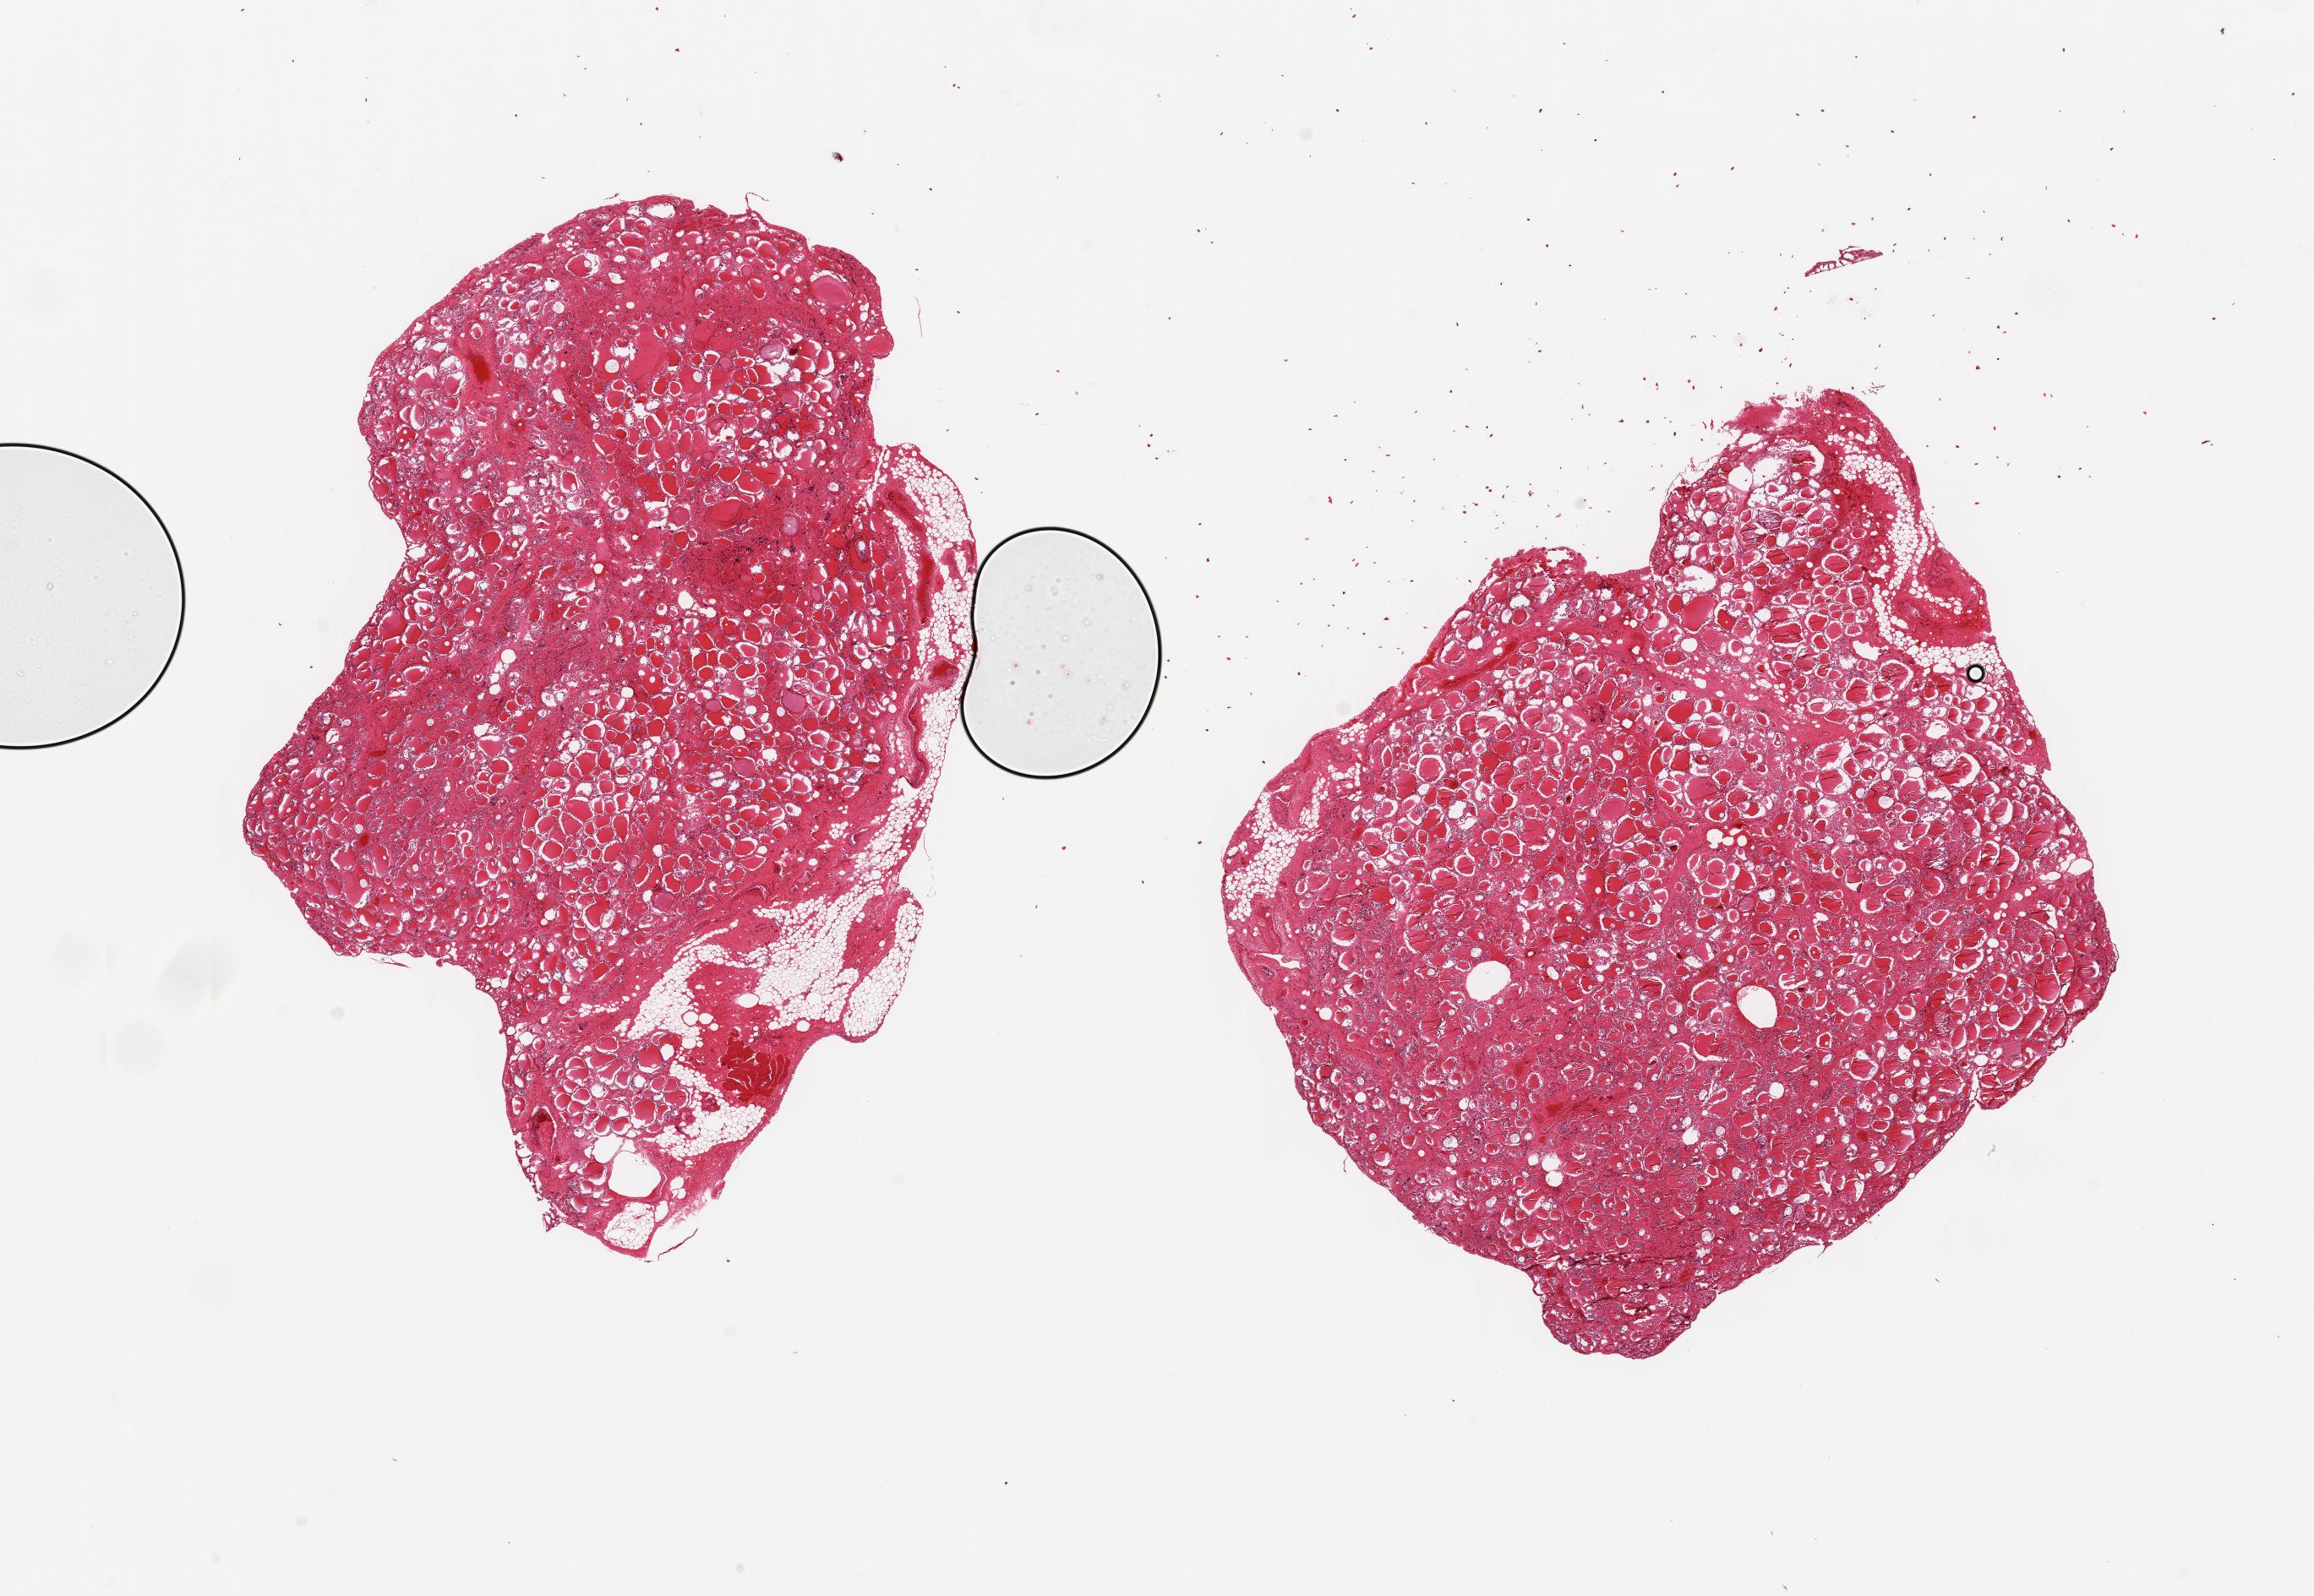
Digitized H&E-stained section, whole scanned area (about 21.7 x 14.9 mm) shown as a low-resolution overview. PAXgene-fixed paraffin-embedded (PFPE) section. Sampled site (target tissue): thyroid. Donor tissue sample.
Review note (as recorded): 2 pieces, 10x6 & 8x7mm; 10% external adipose.